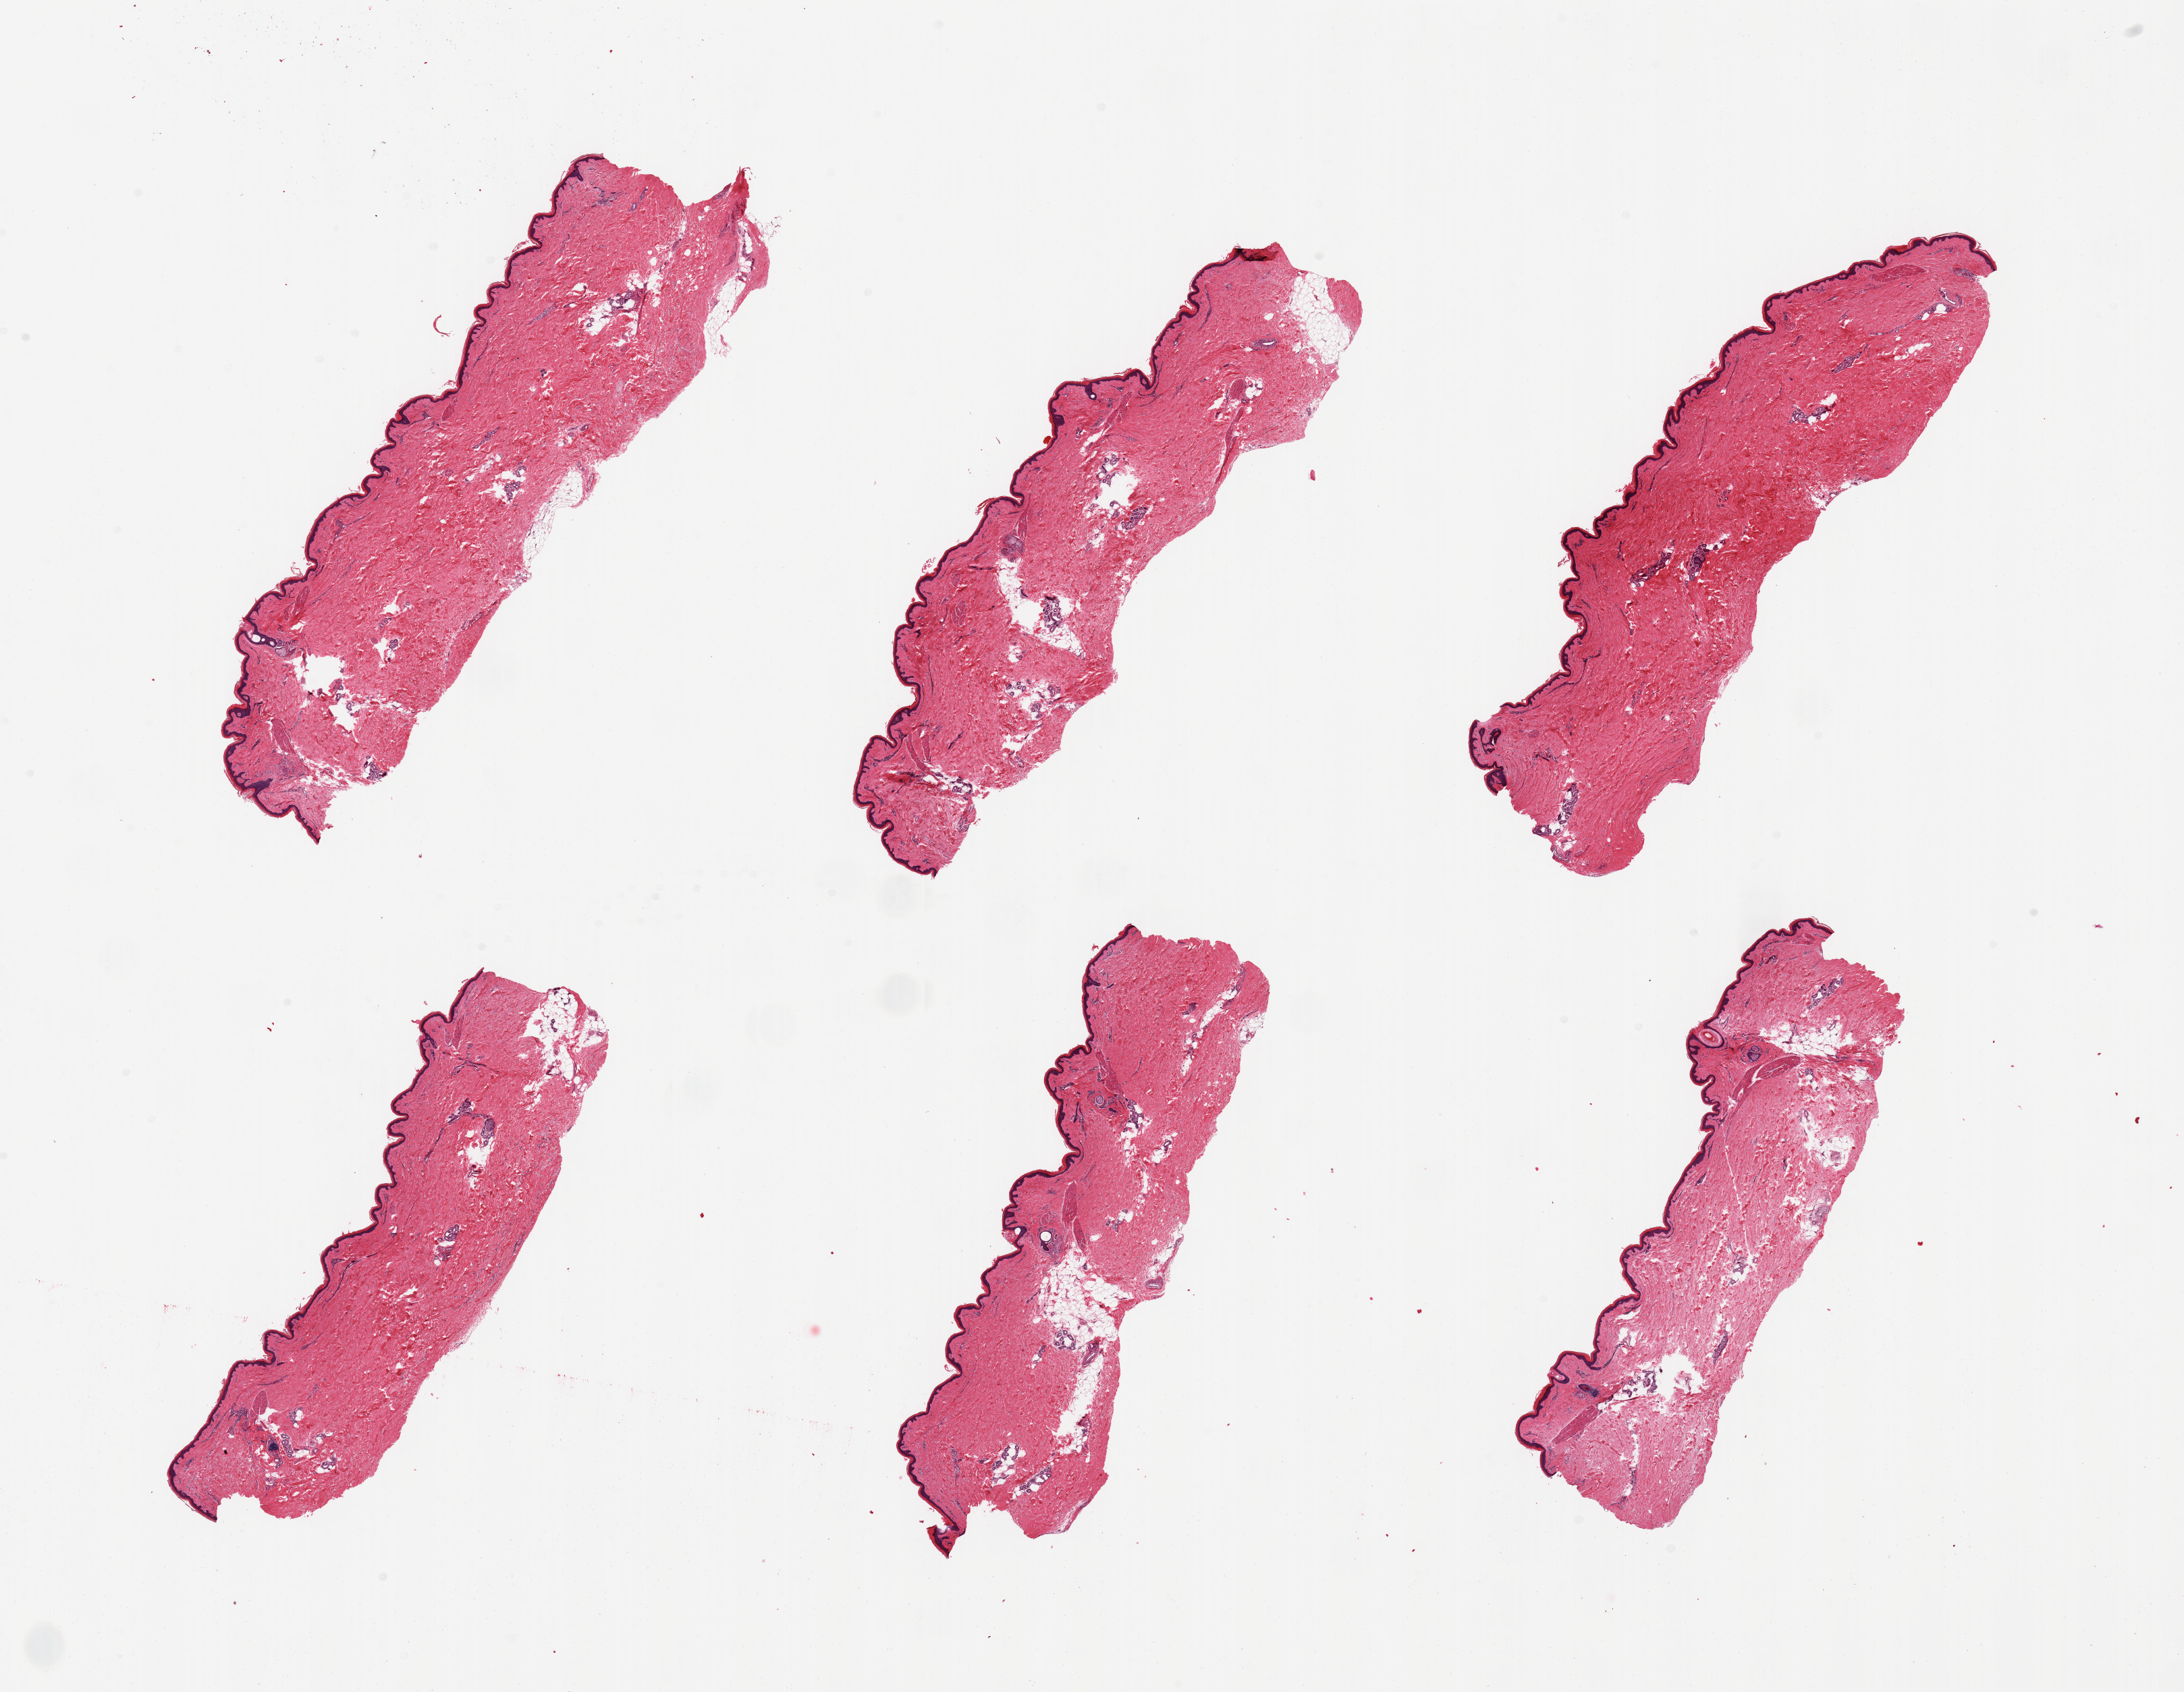
Digitized haematoxylin and eosin-stained section — whole scanned area (about 25.6 x 19.8 mm) shown as a low-resolution overview, PAXgene-fixed paraffin-embedded (PFPE) section, section of skin of lower leg (target tissue), tissue donor sample. Donor: male.
Review note (as recorded): 6 pieces, minimal dermal fat; squamous epithelium is ~35 microns.